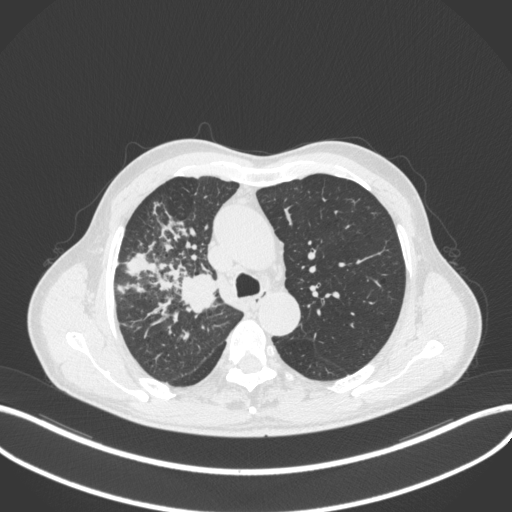
Chest CT, one axial slice. Position 338 of 490 along the scan axis. Reconstruction kernel B31f. 120 kVp. Lung window (W 1500 / L -600 HU). 1 mm slice thickness. 512 × 512 image matrix. Male patient, age 69 years. Case-level facts recorded for this patient, not image findings: clinical TNM (as recorded): T2a N0 M0.
Structures marked on this image (rectangle marked by the reading radiologist):
- lung tumour (recorded histology: adenocarcinoma): bounding box (x1, y1, x2, y2) in pixels: (177, 271, 222, 314)